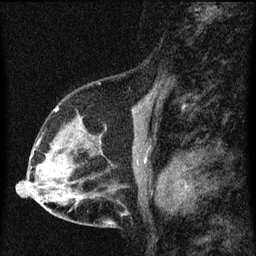
Breast MRI (dynamic contrast-enhanced), one sagittal slice. Slice 38 of 60 in the series (ordered by position). Dynamic contrast-enhanced series, image 2 of 3 at this slice position (ordered by acquisition). 1.5 T. TE 4.2 ms, TR 8 ms. 2 mm slice thickness. 256 × 256 image matrix, field of view 180 × 180 mm. Patient: female, 56 years.
Outlined on this slice (semi-automatic segmentation, software-assisted and operator-edited):
- analysis volume of interest (the breast-tissue region the enhancement analysis was run in; not a lesion): box from (x=34, y=114) to (x=102, y=181) px
- tumour enhancement mask (voxels above the 70 % enhancement threshold inside the analysis volume of interest): (x=47, y=166)–(x=53, y=173)